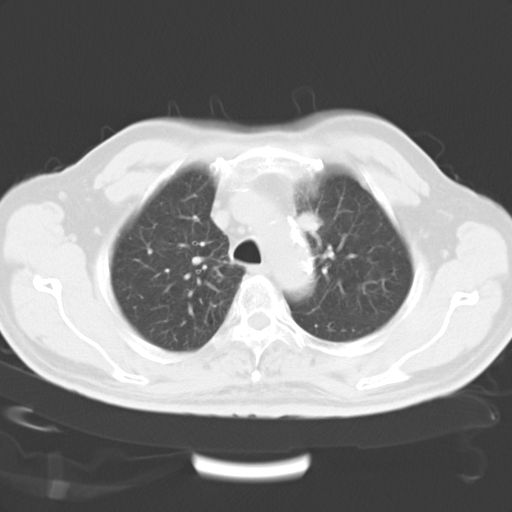
Chest CT, one axial slice. Position 20 of 25 along the scan axis. Lung window (W 1500 / L -600 HU). 10 mm slice thickness. 512 × 512 image matrix, field of view 357 × 357 mm. Patient: male, 67 years. From the clinical record (not read from this slice): clinical TNM (as recorded): T1a N2 M1a.
Outlined on this slice (bounding box drawn by a radiologist):
- lung tumour (recorded histology: large cell carcinoma): bounding box <291,212,321,242> (left, top, right, bottom; pixels)